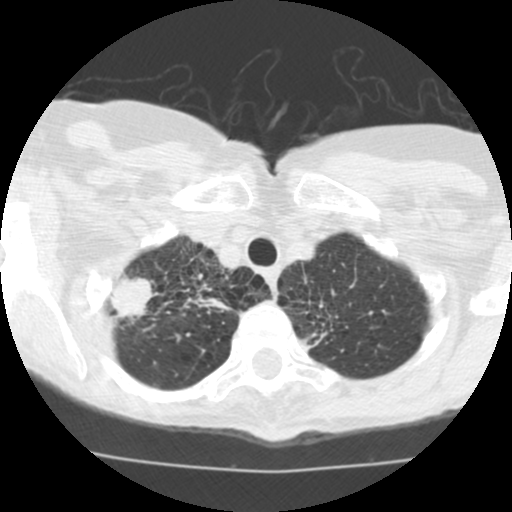
Low-dose screening chest CT, one axial slice. Position 102 of 115 along the scan axis. 120 kVp. Lung window (W 1500 / L -600 HU). 2.5 mm slice thickness. 512 × 512 image matrix.
Outlined on this slice (expert manual segmentation):
- lesion 1 (tumor, upper lobe of right lung): bounding box [x1, y1, x2, y2] px = [110, 276, 153, 317]